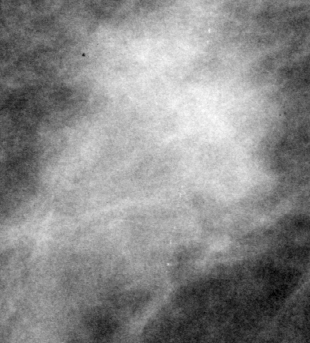
Region of interest cut from a scanned film mammogram (one marked finding); right breast; MLO view; BI-RADS breast density category 2 (scale 1–4).
Marked abnormality: mass, shape irregular, margins microlobulated / ill defined; BI-RADS assessment category 4; subtlety rating 4 on a 1 (subtle) to 5 (obvious) scale; pathology result (as recorded, not read from the image): malignant.